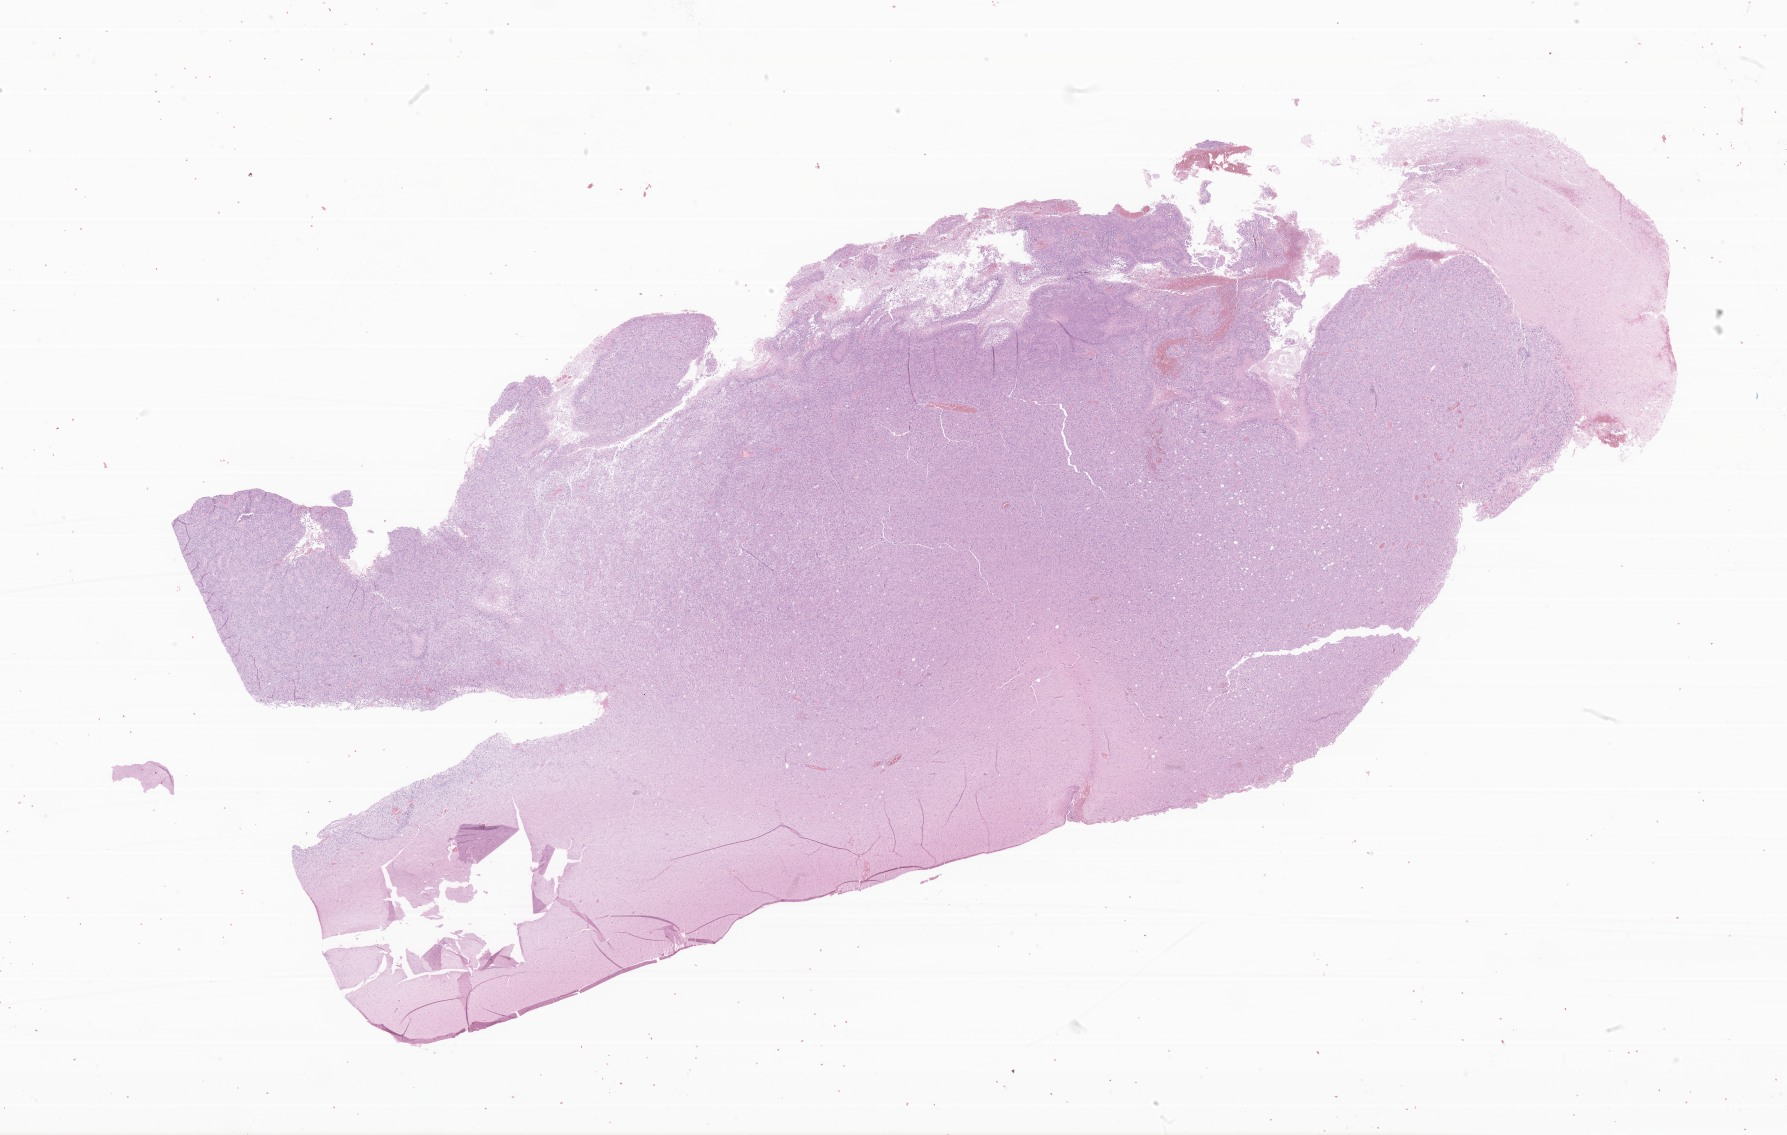
Digitized hematoxylin and eosin (H&E)-stained section of tumor tissue from the temporal lobe — whole scanned area (about 30.1 x 19.1 mm) shown as a low-resolution overview; formalin-fixed, paraffin-embedded (FFPE) tissue. Patient: female, age 50 months.
Diagnosis: Glioblastoma, NOS.